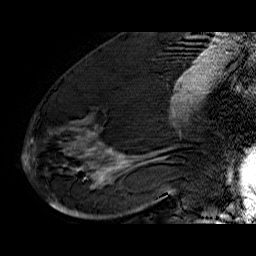
Breast MRI (dynamic contrast-enhanced), one sagittal slice; dynamic contrast-enhanced series, time point 2 of 6 at this slice position (early post-contrast); 1.5 T; TE 6.4 ms, TR 32.9 ms; 4 mm slice thickness; 256 × 256 image matrix, field of view 200 × 200 mm. Female patient. Case-level facts recorded for this patient, not image findings: setting: breast cancer imaged before/during neoadjuvant chemotherapy; receptor status: HR-positive, HER2-negative.
Annotated regions visible in this slice (semi-automatic segmentation, software-assisted and operator-edited):
- analysis volume of interest (the breast-tissue region the enhancement analysis was run in; not a lesion): bounding box <49,74,176,210> (left, top, right, bottom; pixels)
- tumour enhancement mask (voxels above the 100 % enhancement threshold inside the analysis volume of interest): <77,102,176,182>